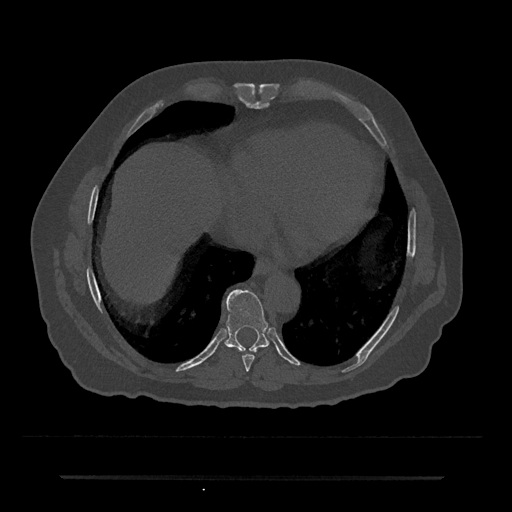
CT including the spine, one axial slice; slice 296 of 797 in the series (ordered by position); bone window (W 1800 / L 400 HU); 512 × 512 image matrix, field of view 437 × 437 mm. Patient: male, 69 years. From the clinical record (not read from this slice): primary cancer: prostate.
Structures marked on this image (semi-automatically segmented with operator editing):
- T8 vertebra: bounding box [x1, y1, x2, y2] px = [242, 354, 255, 371]
- T9 vertebra: [225, 289, 269, 352]